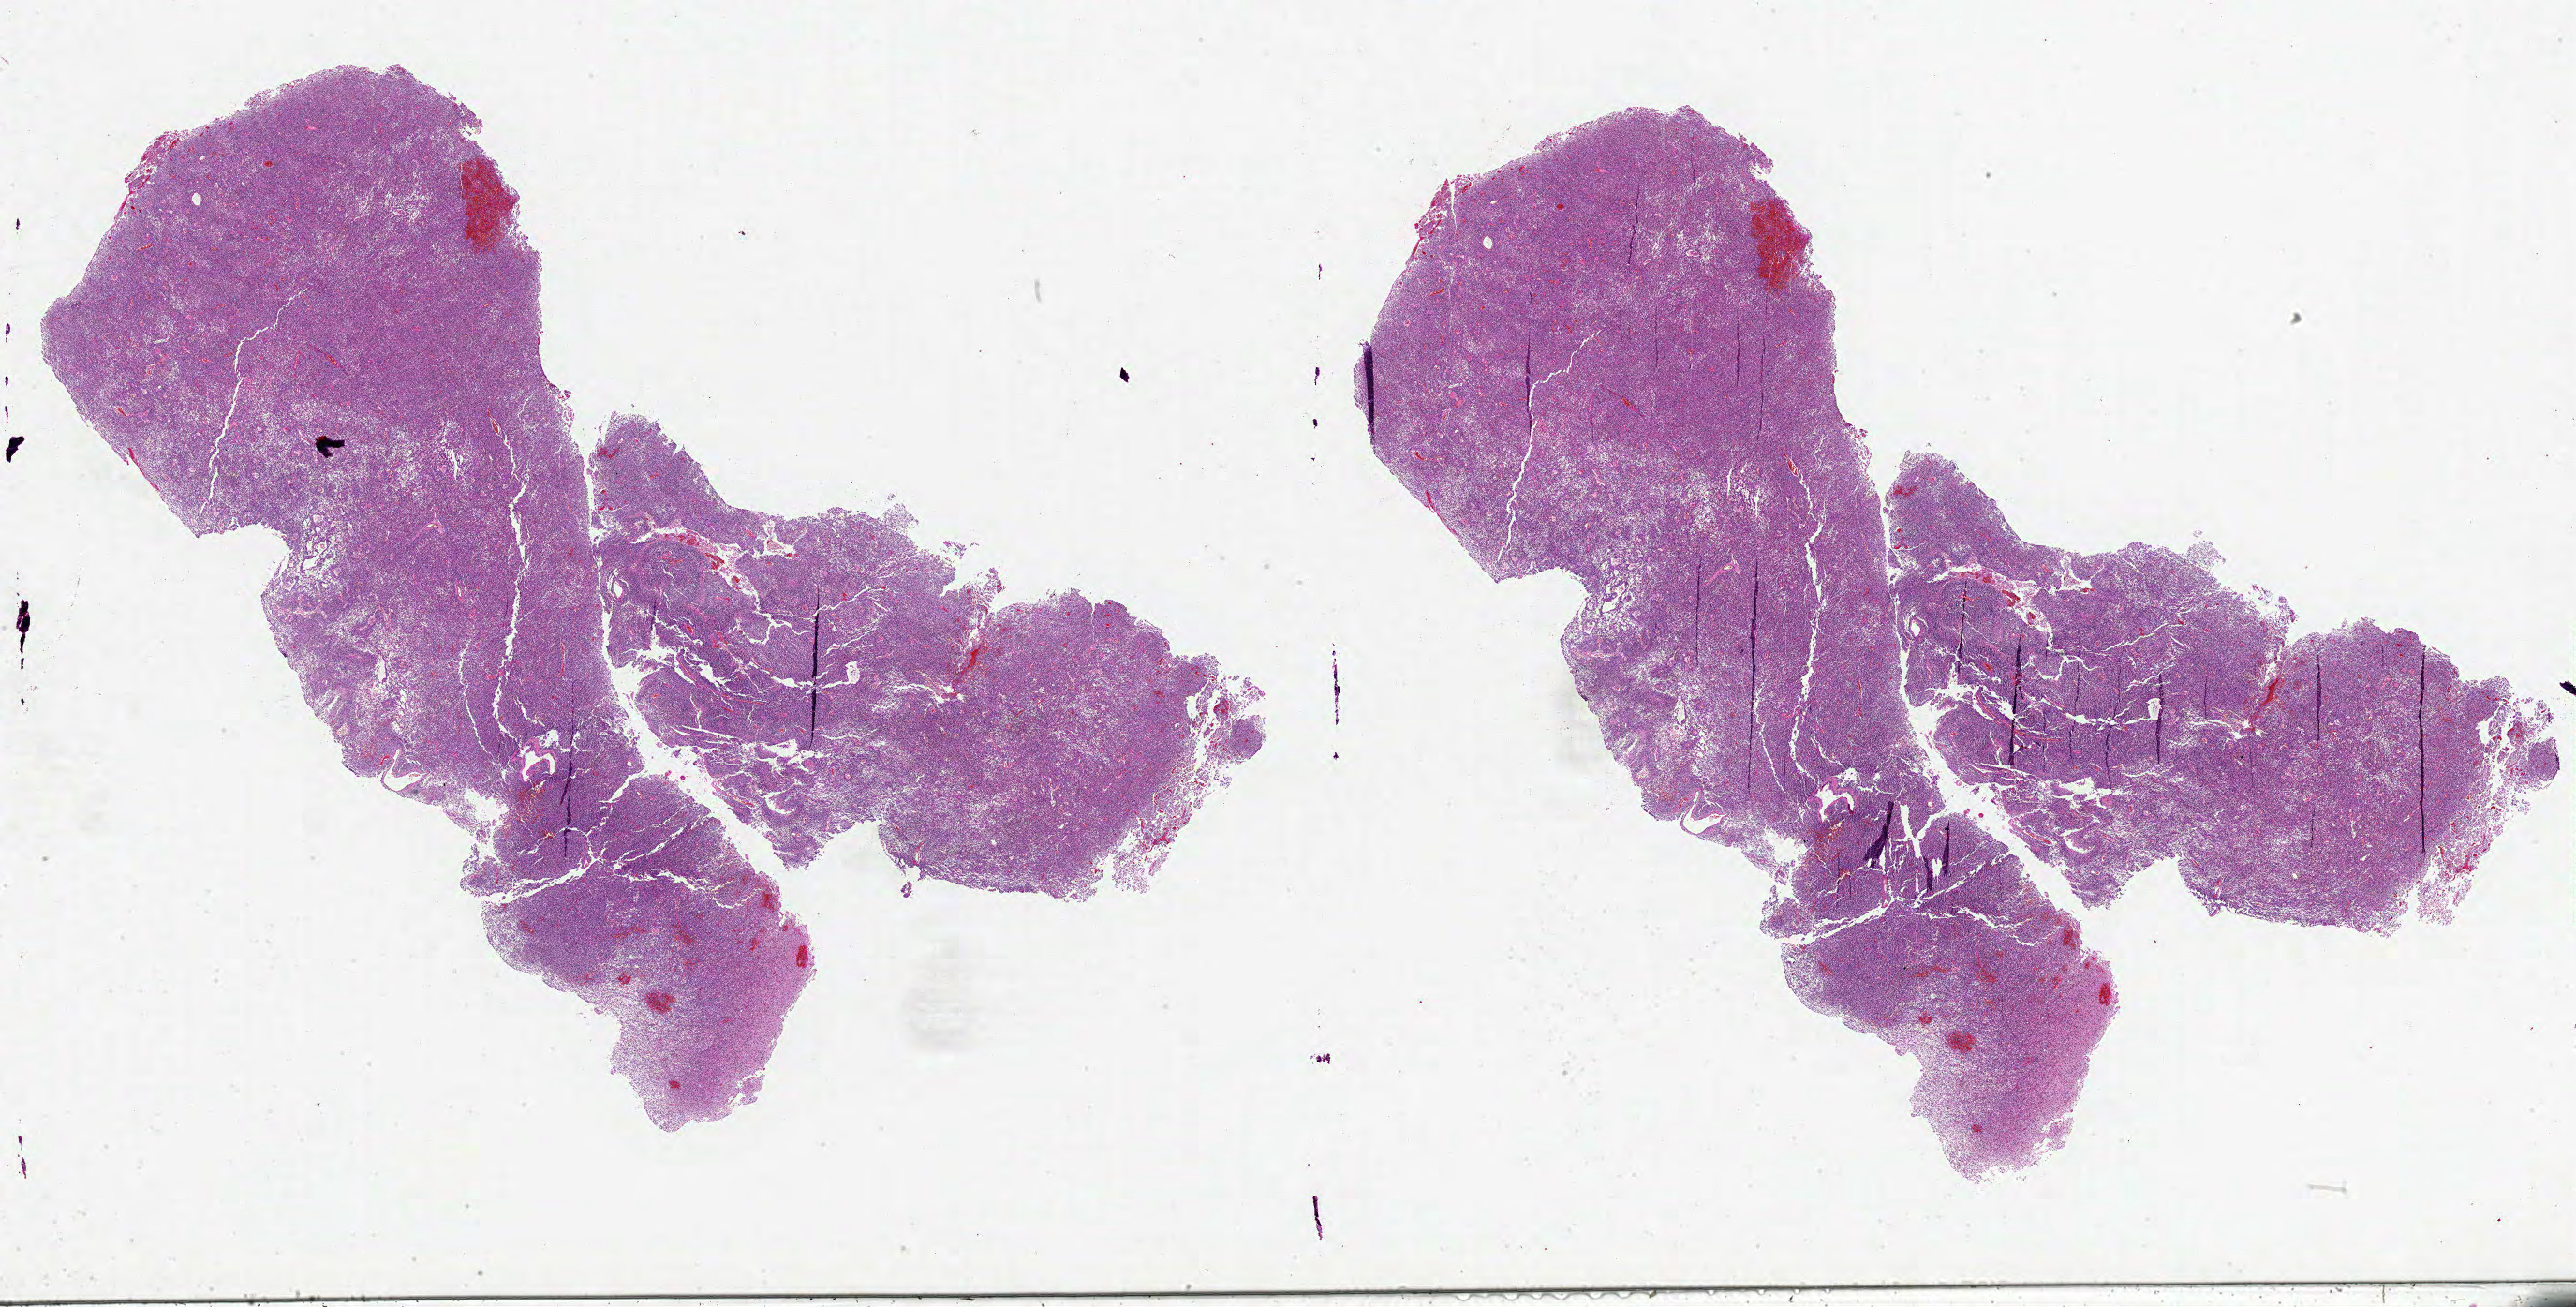
H&E whole-slide image, a low-resolution overview of the entire scanned area, about 44.0 x 22.3 mm, formalin-fixed paraffin-embedded (FFPE) diagnostic section, sample: primary tumour, brain. Female, age 75 years at initial diagnosis.
* pathologic diagnosis: Glioblastoma